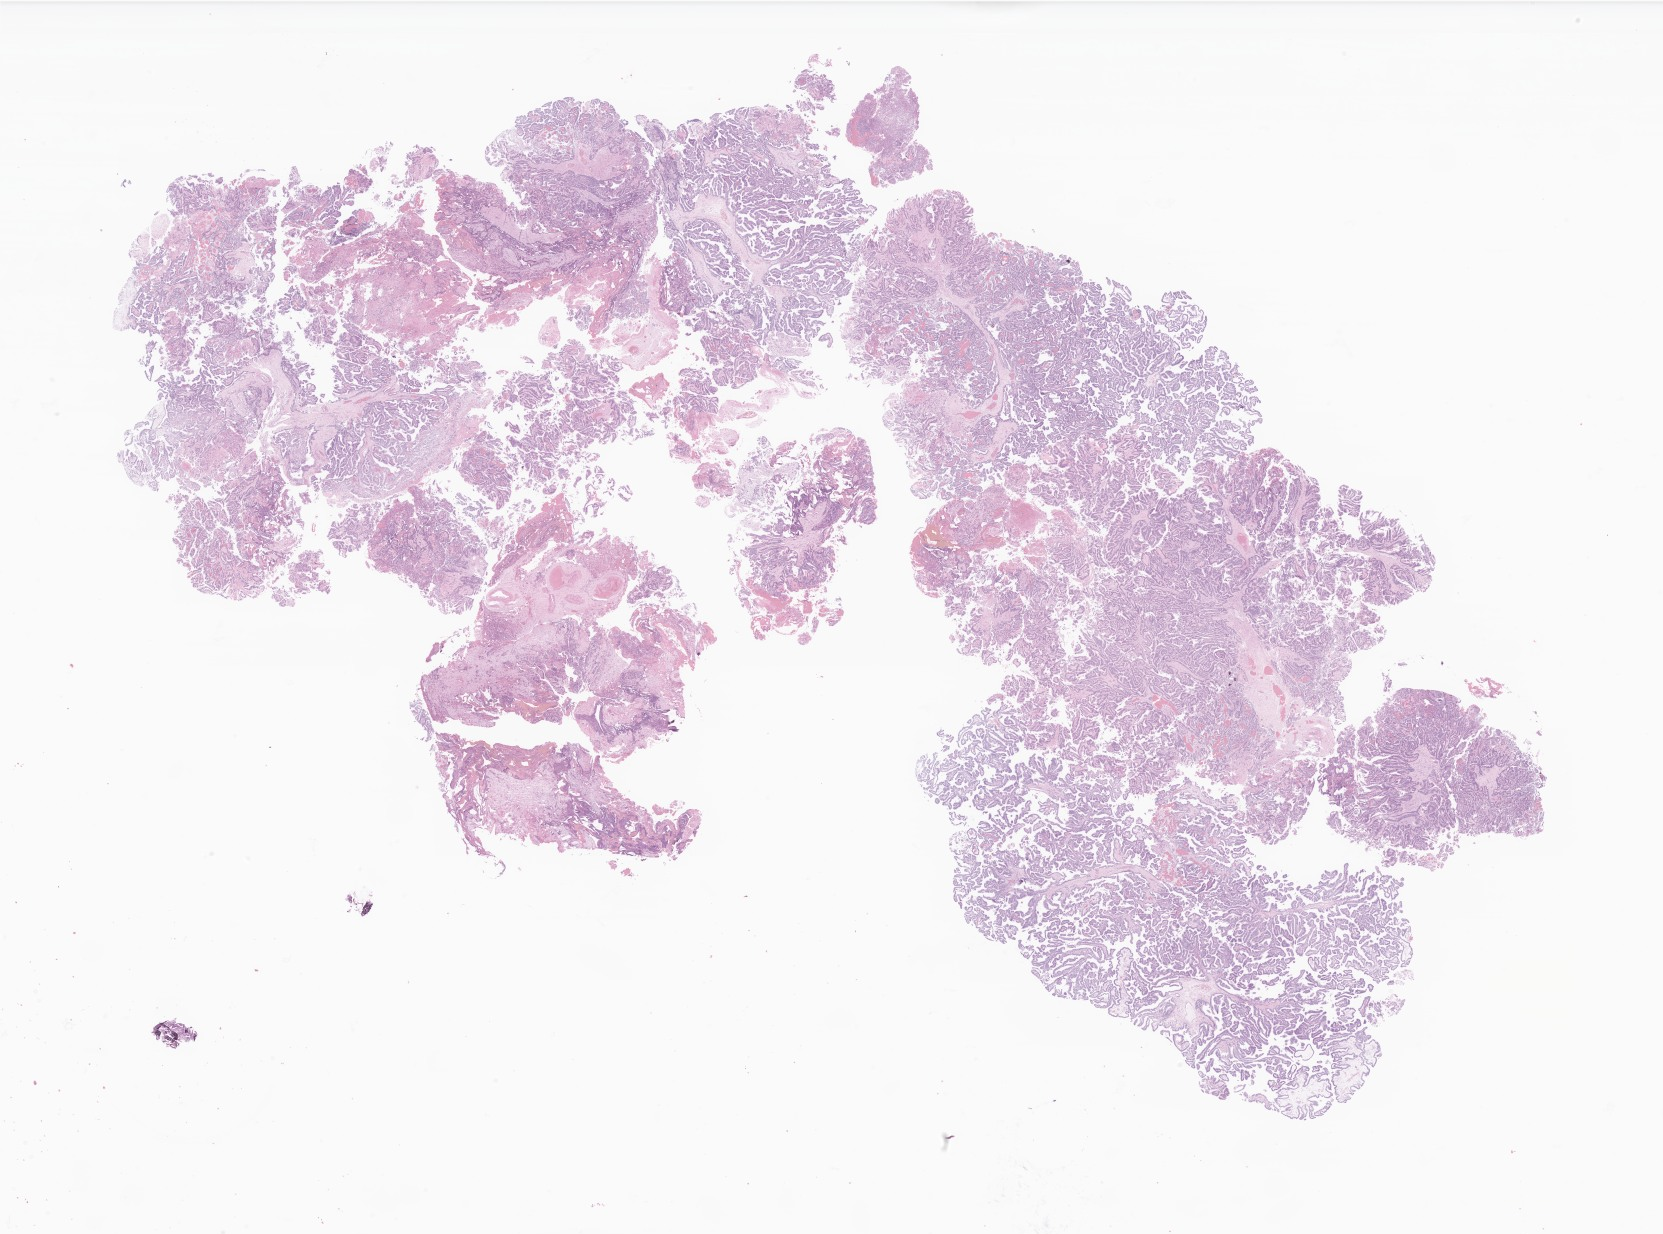
Whole-slide image, haematoxylin and eosin stain of tumor tissue from the brain — whole scanned area (about 28.1 x 20.8 mm) shown as a low-resolution overview. Formalin-fixed paraffin-embedded section. Patient: male, age 429 days (about 1.2 years).
Diagnosis: Neoplasm, malignant.